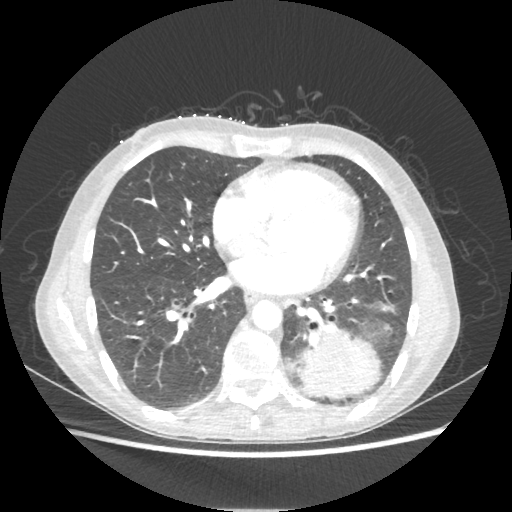
Chest CT, one axial slice. Position 91 of 221 along the scan axis. Reconstruction kernel STANDARD. Lung window (W 1500 / L -600 HU). 1.25 mm slice thickness. 512 × 512 image matrix. Female patient, age 53 years. From the clinical record (not read from this slice): clinical TNM (as recorded): T3 N0 M0.
Outlined on this slice (bounding box drawn by a radiologist):
- lung tumour (recorded histology: adenocarcinoma): bounding box [x1, y1, x2, y2] px = [297, 325, 380, 398]